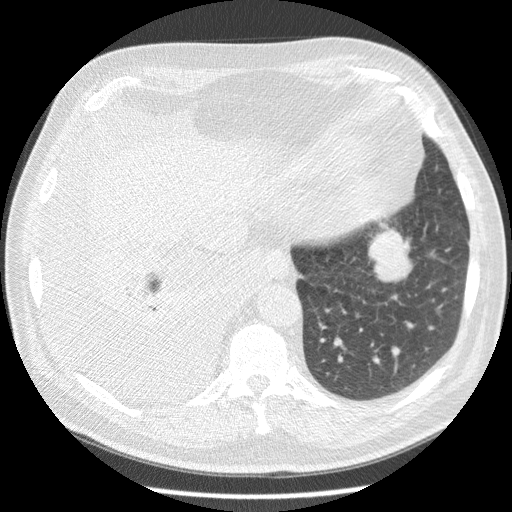
Chest CT (low-dose screening protocol), one axial image; third annual screen; lung window (W 1500 / L -600 HU); standard (soft-tissue) reconstruction kernel (STANDARD); slice 53 of 180 in the series. Male, age 63 years at enrolment.
• Expert-annotated lung lesion, bounding box [x1, y1, x2, y2] px = [358, 217, 421, 282].
• Reader record for this screening exam (exam-level; its link to the box is not recorded): non-calcified nodule or mass ≥4 mm, left lower lobe, 34 × 31 mm, smooth margins, soft tissue attenuation, pre-existing on the prior screen: yes; interval growth: yes.
• Participant outcome: lung cancer diagnosed 30 days after this screen — squamous cell carcinoma, NOS, left lower lobe, stage IB (AJCC 6th edition), 48 mm at pathology.